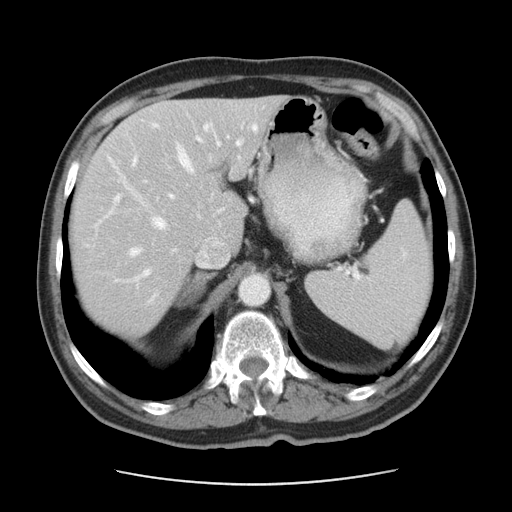
Contrast-enhanced abdominal CT, one axial slice. Position 31 of 42 along the scan axis. Reconstruction kernel STANDARD. 120 kVp. Soft-tissue window (W 400 / L 40 HU). 512 × 512 image matrix, field of view 370 × 370 mm. Male patient, age 73 years. From the clinical record (not read from this slice): diagnosis: colorectal cancer liver metastases, imaged before liver resection; multiple liver metastases: yes; largest metastasis: 0.5 cm.
Outlined on this slice (expert manual segmentation):
- hepatic veins: bounding box [x1, y1, x2, y2] px = [107, 124, 257, 305]
- liver: [71, 96, 280, 333]
- planned liver remnant (the part of the liver to remain after resection): [116, 96, 281, 248]
- portal vein (with intrahepatic branches): [108, 136, 243, 286]